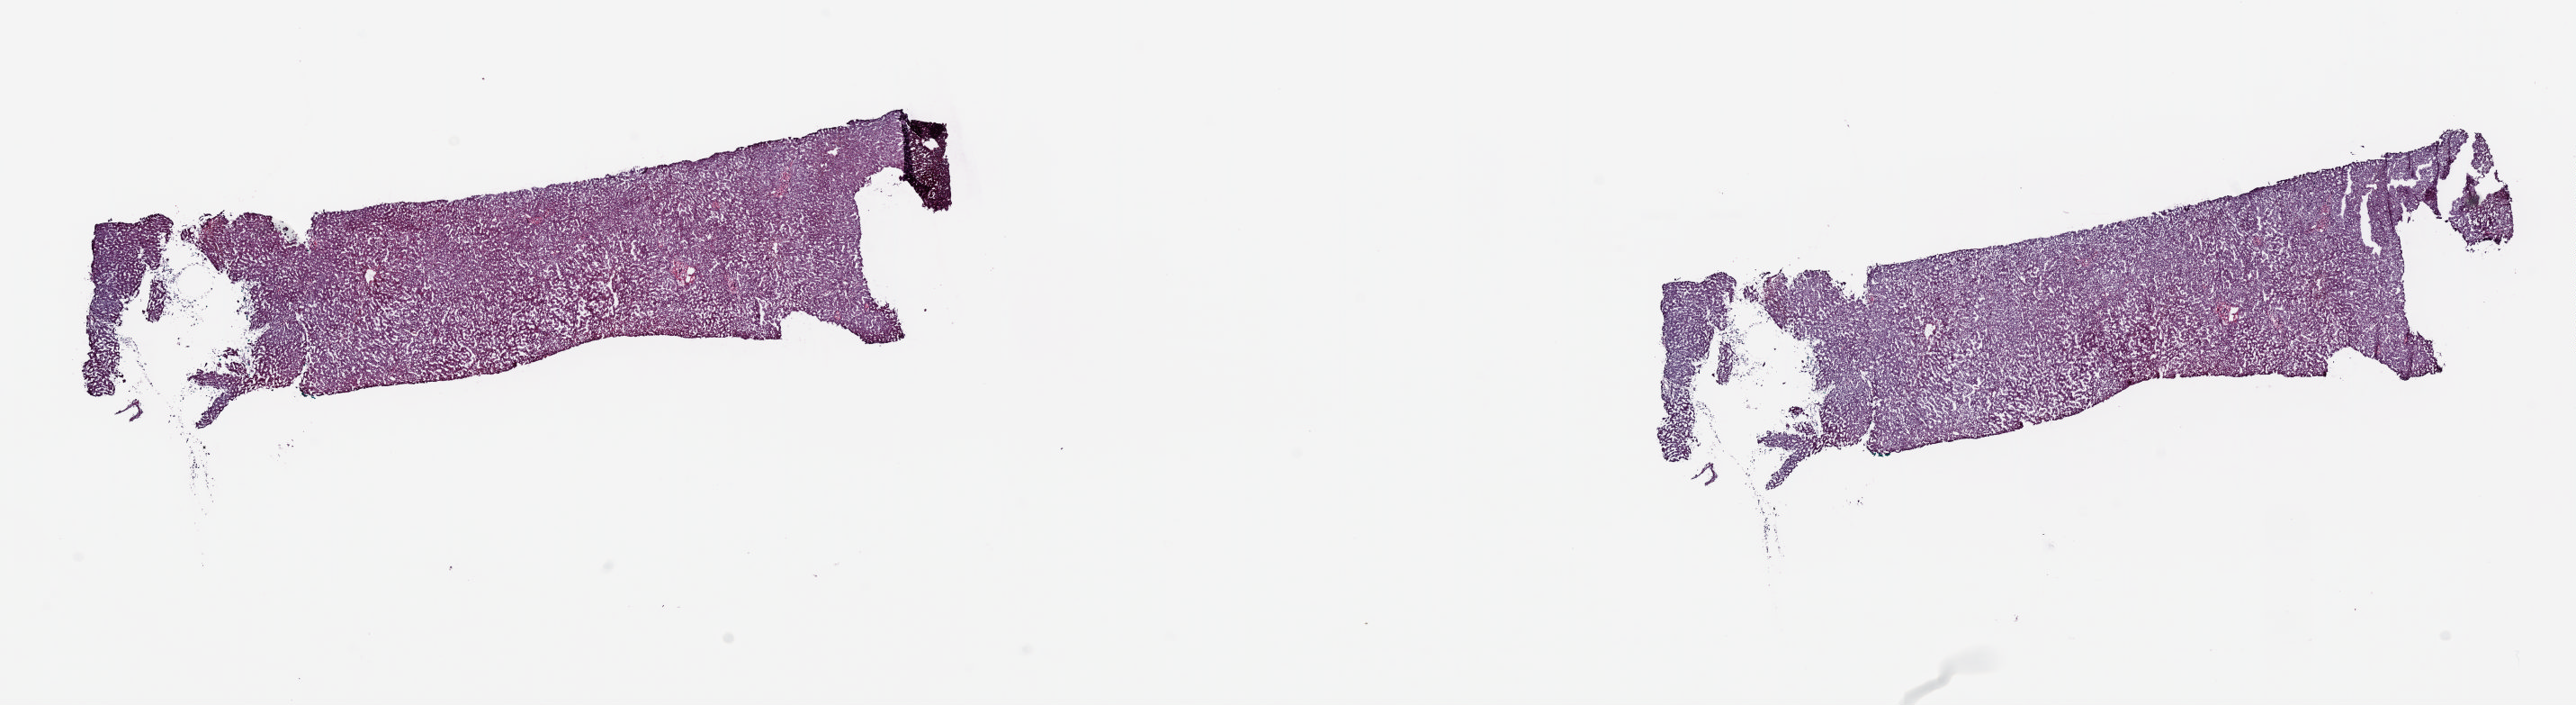
Digitized H&E tissue section (whole slide), low-resolution overview of the scanned area, about 22.6 x 6.2 mm (acquisition: 20x scan), frozen section from the top of the tissue portion, liver, solid tissue normal (non-tumour tissue) sample. Female patient; age at initial diagnosis 76 years. Pathologist review of this section (percent, as recorded): tumour cells 0%, tumour nuclei 0%, normal cells 90%, stromal cells 10%, necrosis 0%. Inflammatory infiltration, as recorded: lymphocyte infiltration 1%, monocyte infiltration 1%, neutrophil infiltration 1%.
This section: solid tissue normal (non-tumour) sample from the same patient. Patient diagnosis: Hepatocellular carcinoma, fibrolamellar.